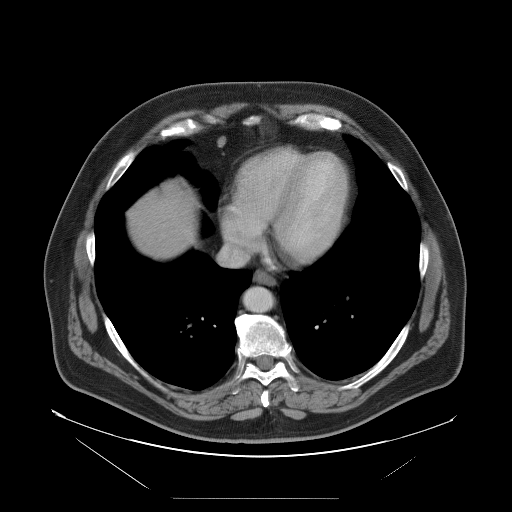
Contrast-enhanced abdominal CT, one axial slice. Position 97 of 114 along the scan axis. Intravenous contrast given. Soft-tissue window (W 400 / L 40 HU). 5 mm slice thickness. 512 × 512 image matrix, field of view 500 × 500 mm. Male patient, age 61 years. From the clinical record (not read from this slice): diagnosis: colorectal cancer liver metastases, imaged before liver resection; multiple liver metastases: no; largest metastasis: 6.5 cm; disease in both lobes: yes.
Outlined on this slice (manually delineated by an expert):
- hepatic veins: bounding box [x1, y1, x2, y2] px = [221, 214, 268, 267]
- liver: [130, 187, 195, 256]
- planned liver remnant (the part of the liver to remain after resection): [170, 184, 196, 222]